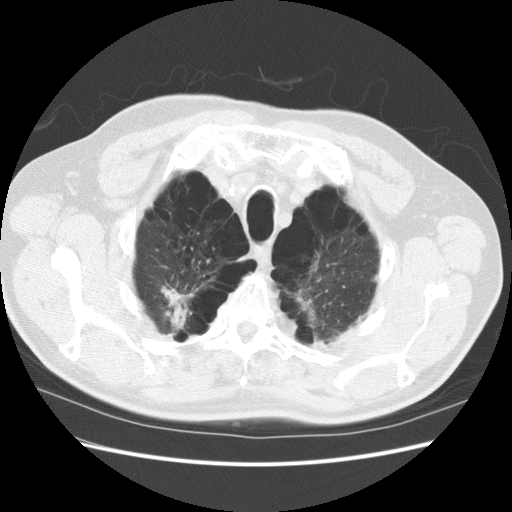
Low-dose screening chest CT, axial slice, baseline screening round, lung window (W 1500 / L -600 HU), 2.5 mm slice thickness. Male participant, aged 68 years at enrolment. Former smoker at enrolment.
Lesion marked by an expert reader, bounding box [x1, y1, x2, y2] px = [121, 272, 219, 339]. The screening reader recorded 2 non-calcified nodules or masses ≥4 mm on this exam; which of them this box marks is not recorded. Official screen result: positive, change unspecified: nodule(s) >= 4 mm or enlarging nodule(s), mass(es), or other non-specific abnormalities suspicious for lung cancer. Later outcome: lung cancer diagnosed 1003 days after this screen — large cell carcinoma, NOS, right upper lobe, poorly differentiated (G3), stage IV (AJCC 6th edition).